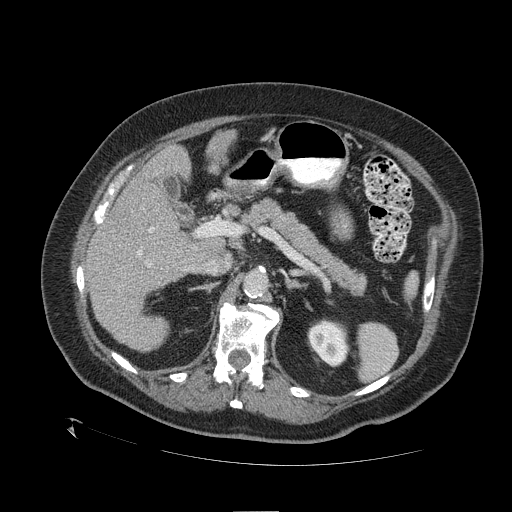
Contrast-enhanced abdominal CT (liver protocol), one axial slice; position 64 of 109 along the scan axis; reconstruction kernel STANDARD; one of 2 acquisitions stored at this slice position; soft-tissue window (W 400 / L 40 HU); 2.5 mm slice thickness; 512 × 512 image matrix. From the clinical record (not read from this slice): diagnosis: hepatocellular carcinoma (patient treated with transarterial chemoembolisation; whether this scan precedes or follows treatment is not stated here); TNM stage (as recorded): Stage-I; Child-Pugh class: A; tumour differentiation: no biopsy; tumour size: 4.6 cm.
Annotated regions visible in this slice (semi-automatically segmented with operator editing):
- liver parenchyma outside the tumour (the mass and vessels are separate outlines, so this box may not span the whole liver): box from (x=86, y=130) to (x=236, y=352) px
- liver vessels: (x=103, y=218)–(x=214, y=267)